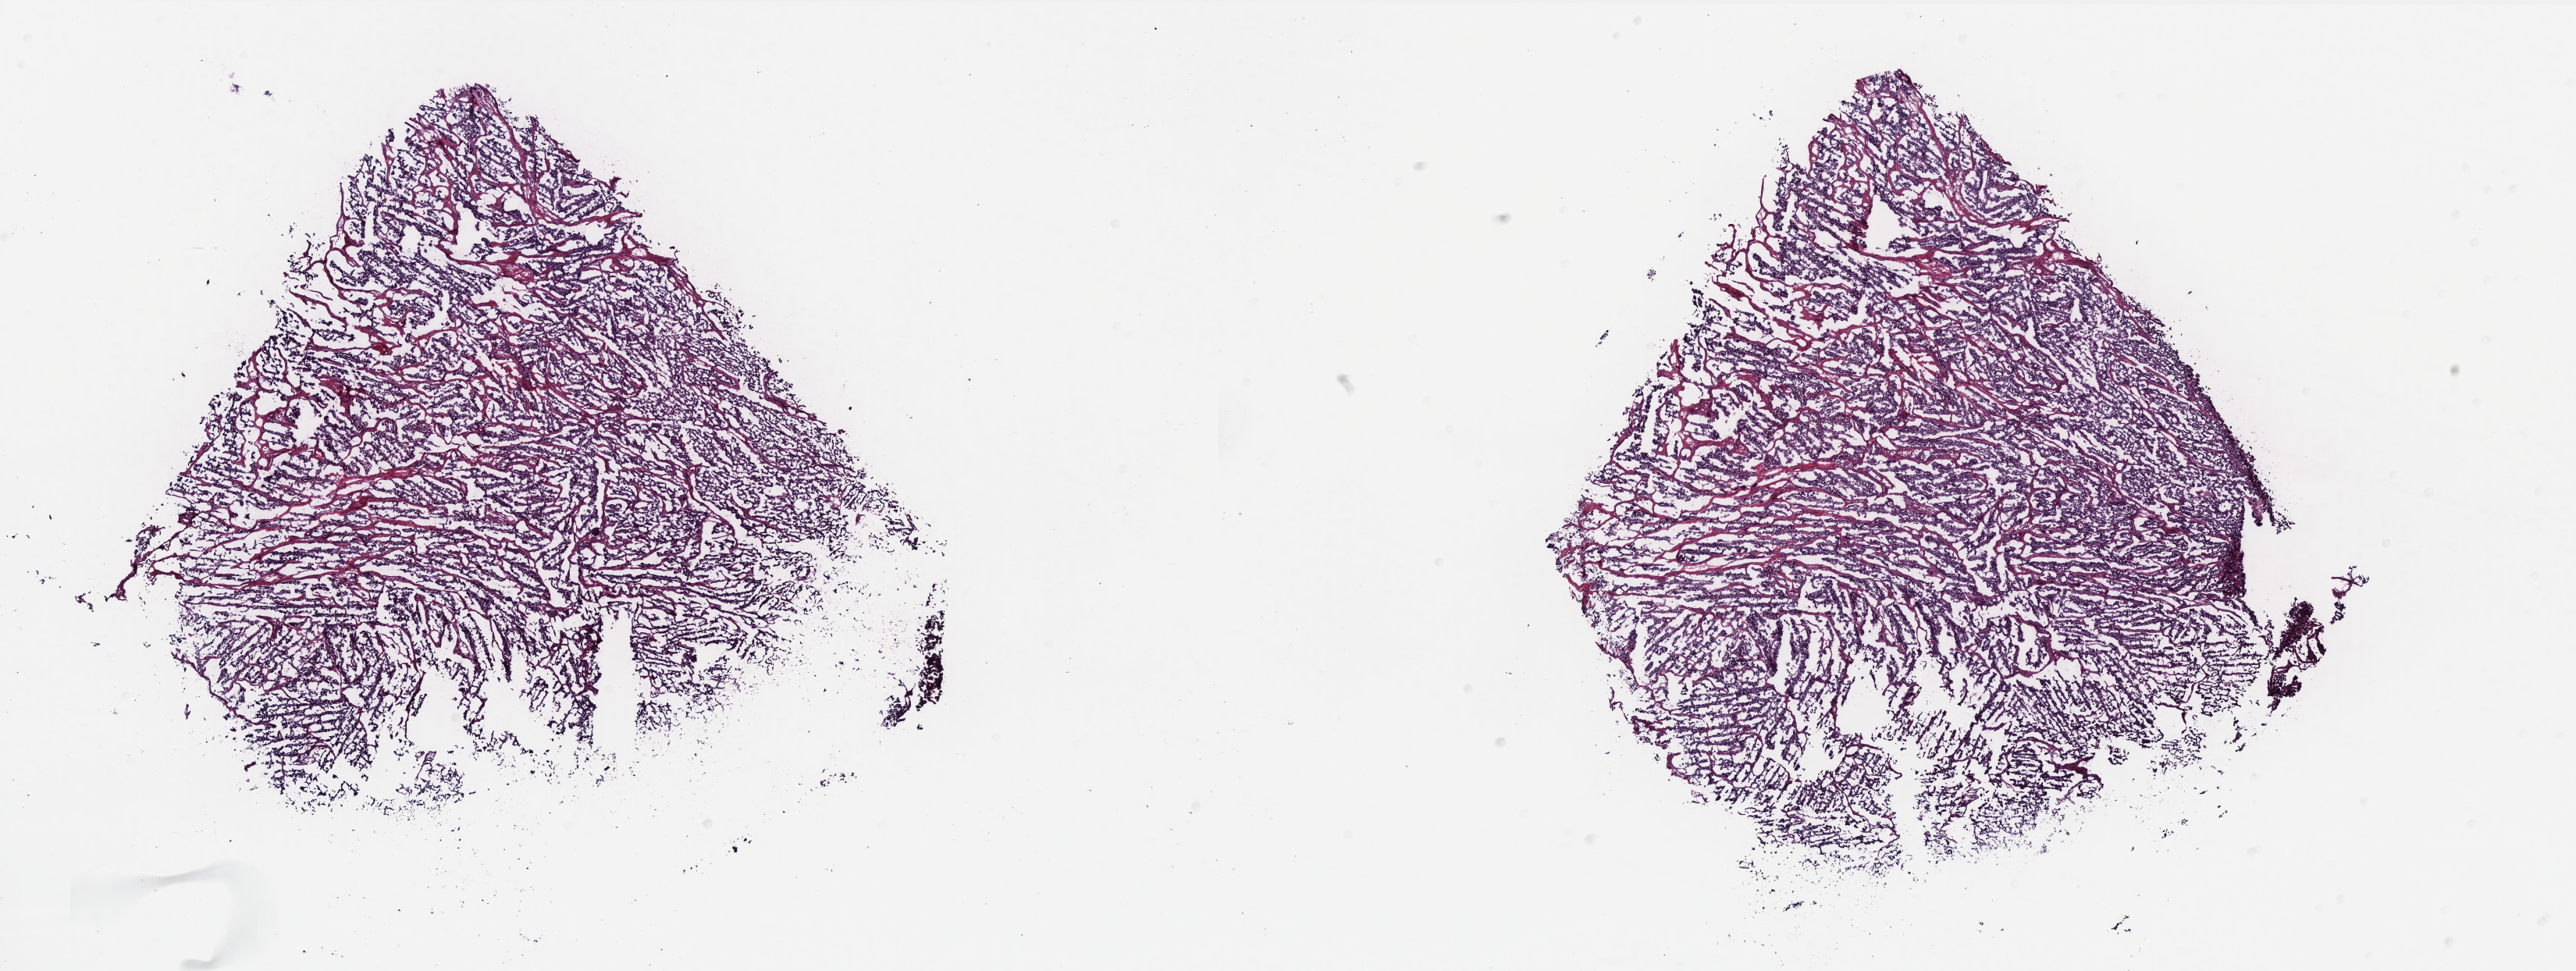
Whole-slide histology image, Hematoxylin and eosin (H&E) stained — shown as a low-resolution overview of the whole scanned area (about 26.5 x 10.0 mm); frozen section from the bottom of the tissue portion; sample: primary tumour, uterus. Patient: female, age at initial diagnosis 63 years. Histologic grade: G3 (poorly differentiated). Composition of this section per pathologist review: tumour cells 80%, tumour nuclei 90%, normal cells 10%, stromal cells 0%, necrosis 10%. Infiltration values recorded for this section: lymphocyte infiltration 10%, monocyte infiltration 0%, neutrophil infiltration 10%.
Lymph nodes positive (case pathology): 0 of 20 examined. FIGO stage: IB. Histologic diagnosis: Endometrioid adenocarcinoma, NOS (endometrium).